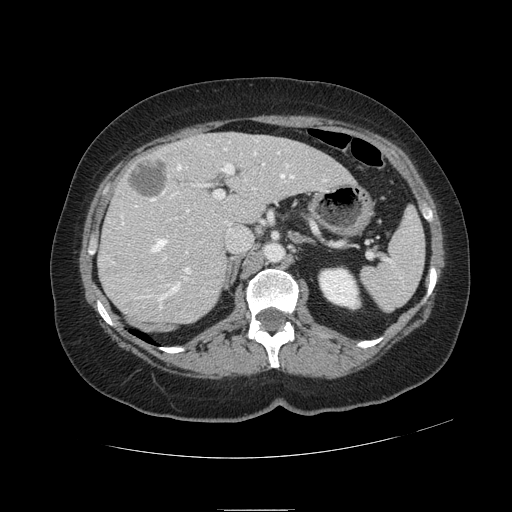
Contrast-enhanced abdominal CT, one axial slice. Position 65 of 121 along the scan axis. 120 kVp. Intravenous contrast given. Soft-tissue window (W 400 / L 40 HU). 2.5 mm slice thickness. 512 × 512 image matrix, field of view 400 × 400 mm. Female patient, age 52 years. Case-level facts recorded for this patient, not image findings: diagnosis: colorectal cancer liver metastases, imaged before liver resection; multiple liver metastases: yes; largest metastasis: 6.3 cm.
Annotated regions visible in this slice (manually delineated by an expert):
- hepatic veins: bounding box (x1, y1, x2, y2) in pixels: (135, 142, 327, 309)
- liver: (100, 133, 352, 324)
- planned liver remnant (the part of the liver to remain after resection): (167, 134, 353, 223)
- portal vein (with intrahepatic branches): (122, 151, 280, 274)
- liver metastasis: (129, 160, 167, 196)